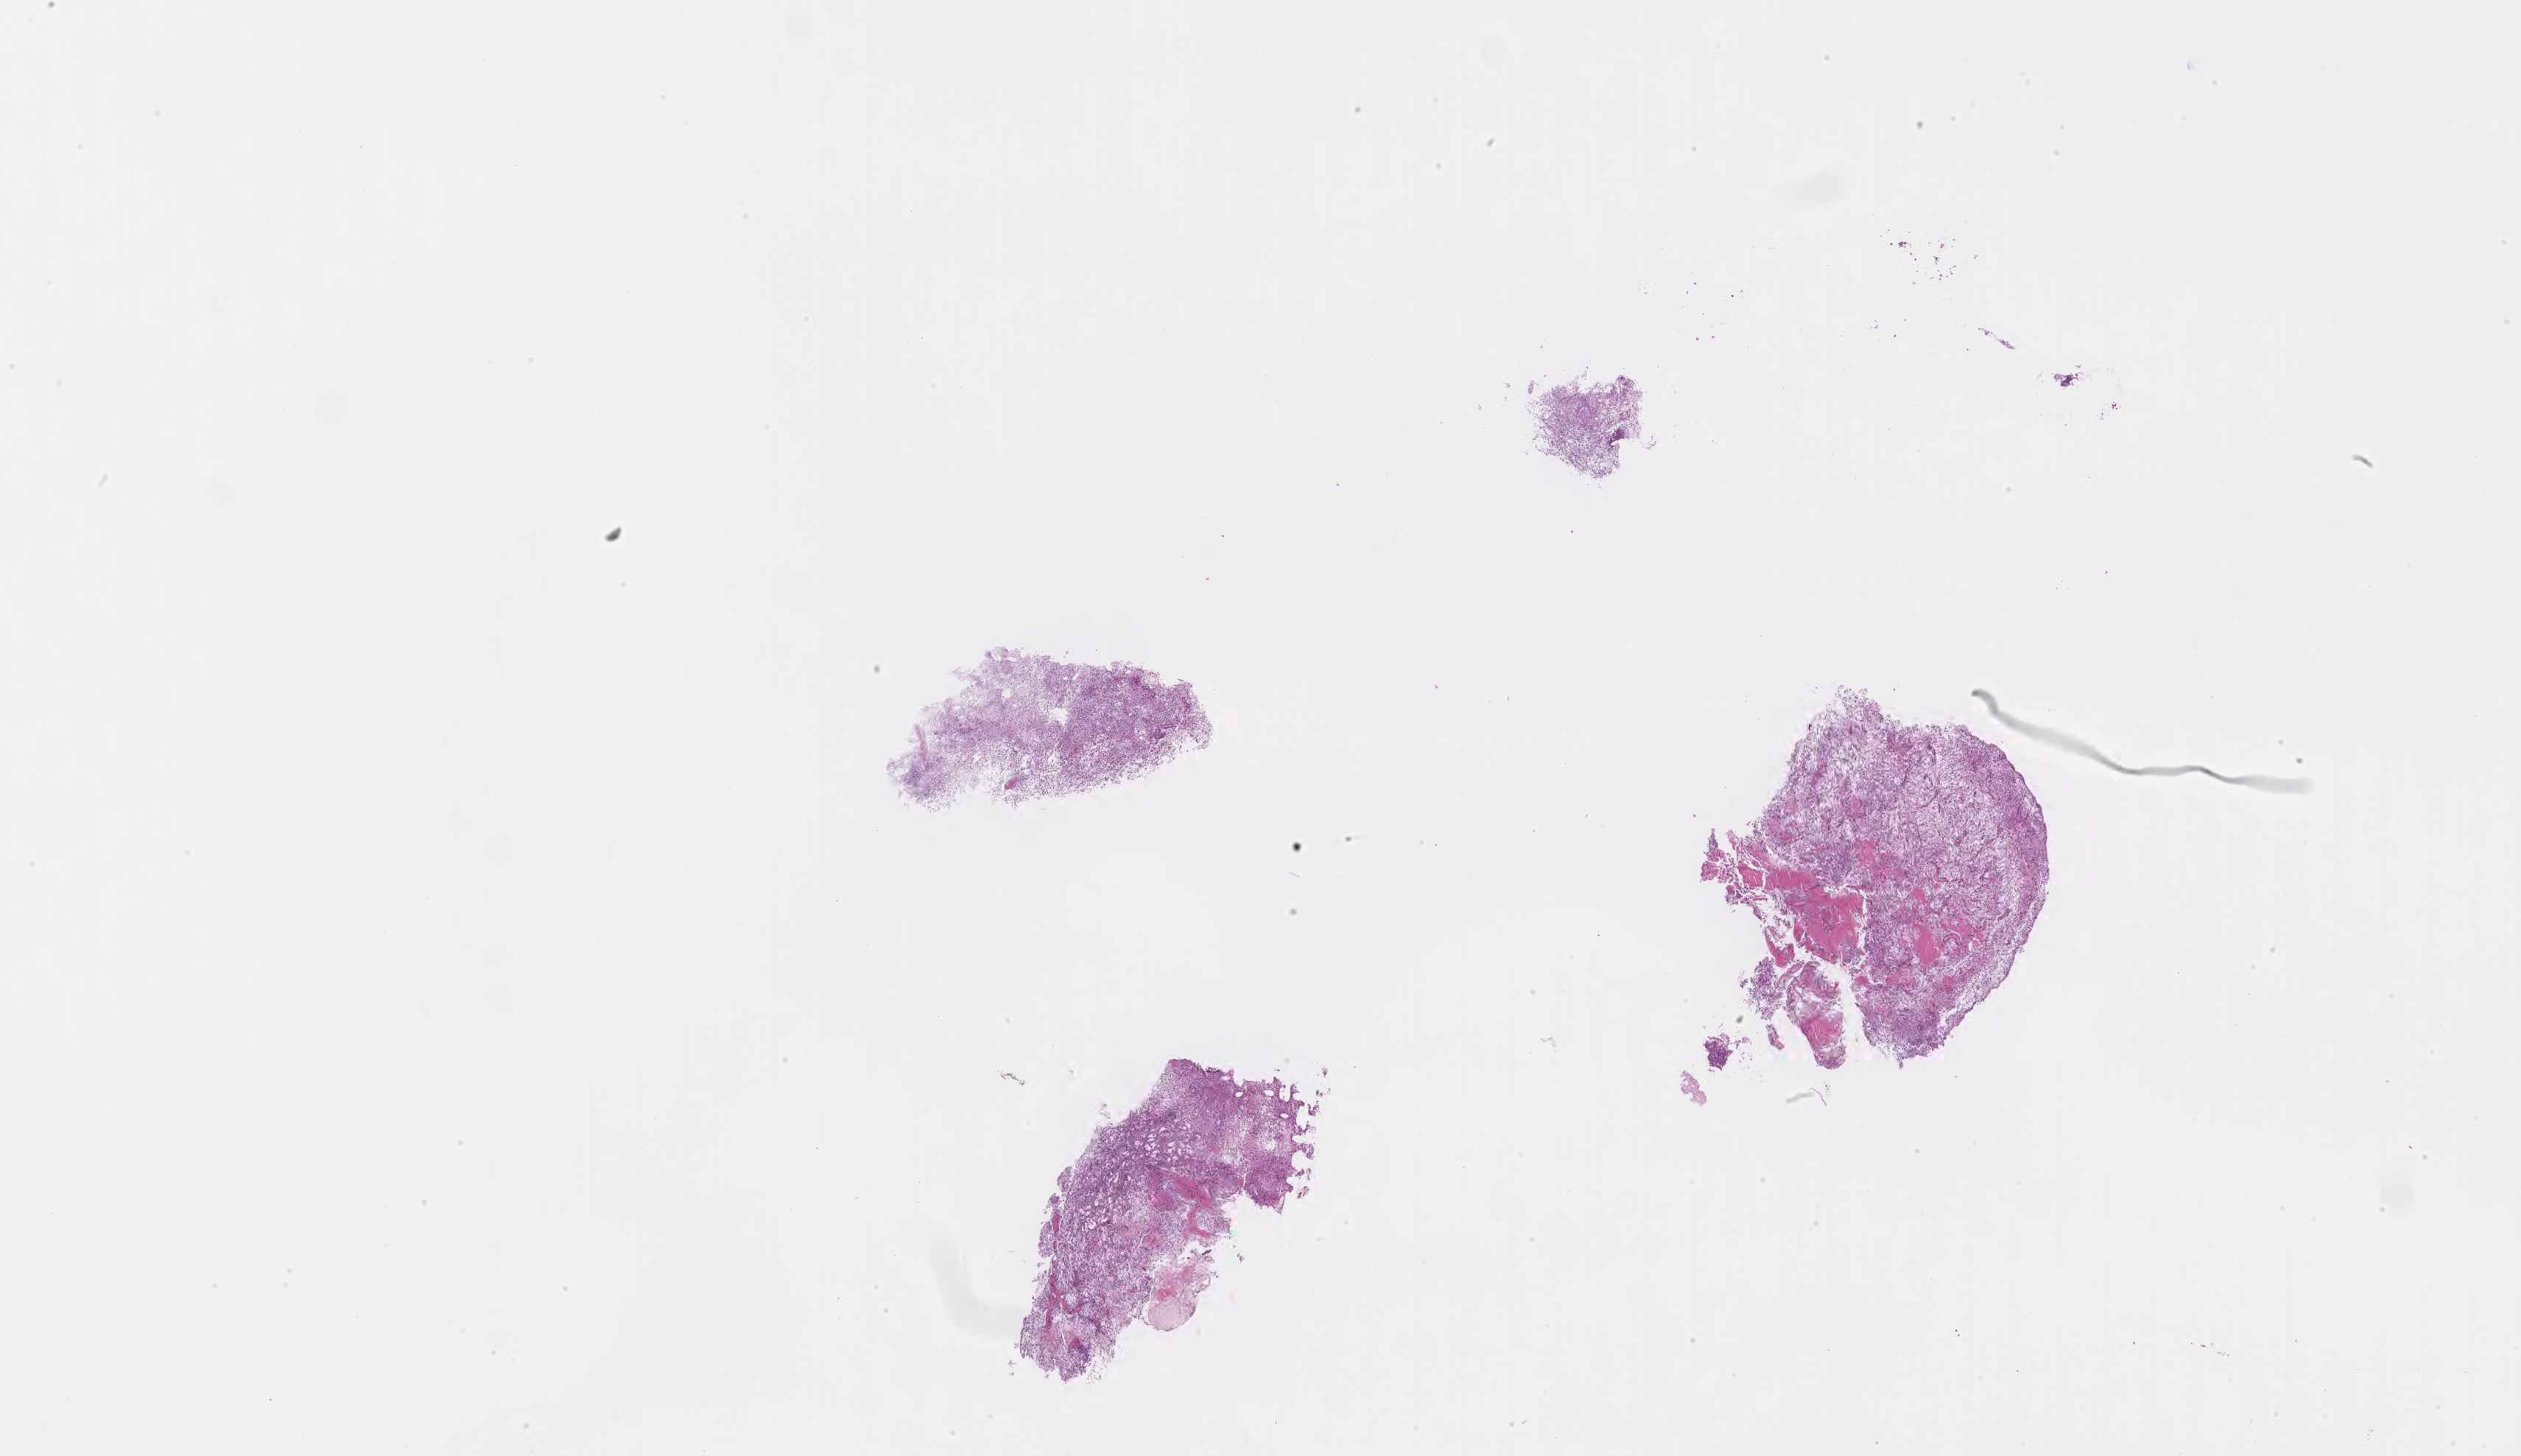
Digitized haematoxylin and eosin-stained section of tumor tissue from the brain stem, low-resolution overview of the scanned area, about 27.7 x 16.0 mm, formalin-fixed paraffin-embedded section. Patient female; age 52 months (4 years 4 months).
- diagnosis (ICD-O-3 morphology term): Pilocytic astrocytoma